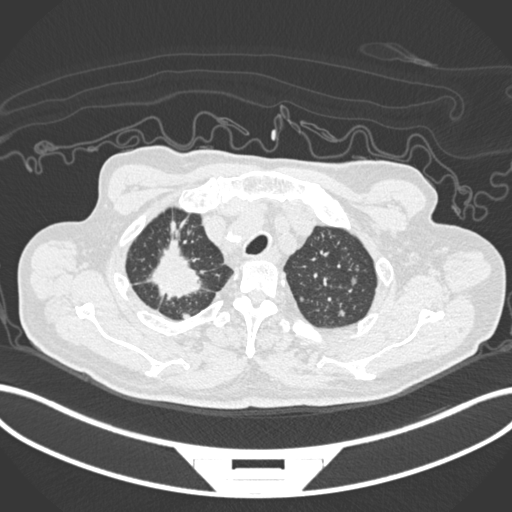
Chest CT, one axial slice. Position 188 of 207 along the scan axis. Reconstruction kernel B30f. 120 kVp. Lung window (W 1500 / L -600 HU). 1 mm slice thickness. 512 × 512 image matrix. Male patient, age 69 years. From the clinical record (not read from this slice): clinical TNM (as recorded): T1c N1 M1.
Annotated regions visible in this slice (bounding box drawn by a radiologist):
- lung tumour (recorded histology: adenocarcinoma): bounding box [x1, y1, x2, y2] px = [148, 238, 208, 303]